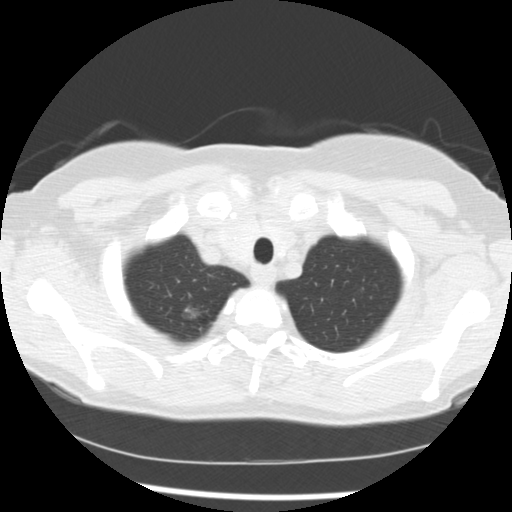
Low-dose screening chest CT, axial slice, baseline annual screen, lung window (W 1500 / L -600 HU). Female participant, aged 60 years at enrolment. Former smoker at enrolment.
Lesion marked by an expert reader, bounding box (x1, y1, x2, y2) in pixels: (170, 294, 208, 330). The screening reader recorded 3 non-calcified nodules or masses ≥4 mm on this exam (right upper lobe, right middle lobe, left lower lobe); which of them this box marks is not recorded. Official screen result: positive, change unspecified: nodule(s) >= 4 mm or enlarging nodule(s), mass(es), or other non-specific abnormalities suspicious for lung cancer. Lung cancer was diagnosed 100 days after this screen: bronchiolo-alveolar adenocarcinoma, NOS, right upper lobe, moderately differentiated (G2), stage IA (AJCC 6th edition), 9 mm at pathology.